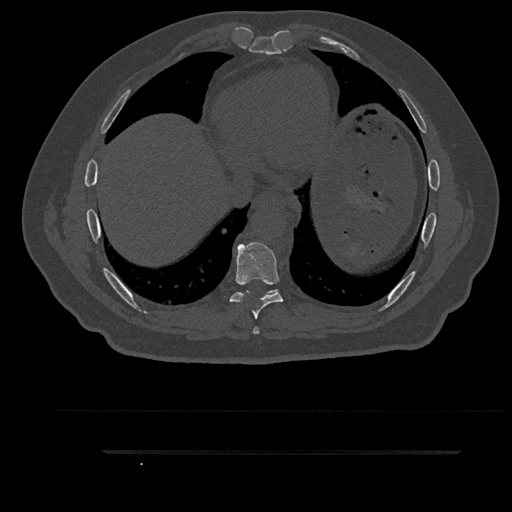
CT including the spine, one axial slice. Reconstruction kernel Br40s/3. Bone window (W 1800 / L 400 HU). 512 × 512 image matrix, field of view 432 × 432 mm. Patient: male, 63 years. From the clinical record (not read from this slice): primary cancer: renal; vertebrae with lytic lesions (as recorded): T8.
Outlined on this slice (semi-automatic segmentation, software-assisted and operator-edited):
- T7 vertebra: bounding box (x1, y1, x2, y2) in pixels: (253, 326, 260, 334)
- T8 vertebra: (230, 242, 283, 319)
- T9 vertebra: (246, 291, 275, 294)